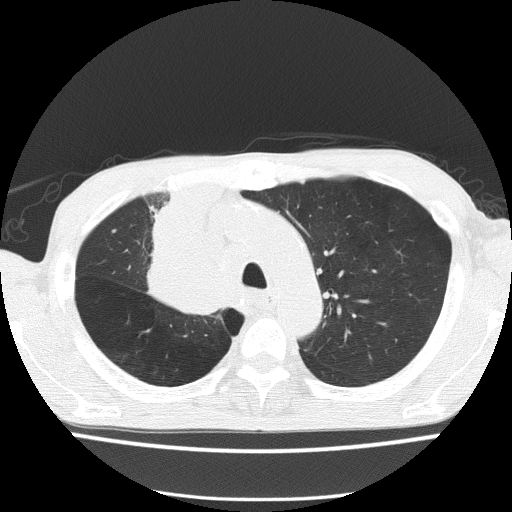
Low-dose screening chest CT, axial slice, first (baseline) screen, lung window (W 1500 / L -600 HU), 2 mm slice thickness, 120 kVp, 512 × 512 image matrix. Male participant, aged 59 years at enrolment. Former smoker at enrolment.
Expert reader's lesion annotation, bounding box (x1, y1, x2, y2) in pixels: (133, 233, 237, 325). The screening reader recorded 5 non-calcified nodules or masses ≥4 mm on this exam (left upper lobe, left upper lobe, left upper lobe, right middle lobe, right lower lobe); which of them this box marks is not recorded. Participant outcome: lung cancer diagnosed 72 days after this screen — squamous cell carcinoma, NOS, right upper lobe, moderately differentiated (G2), stage IV (AJCC 6th edition).